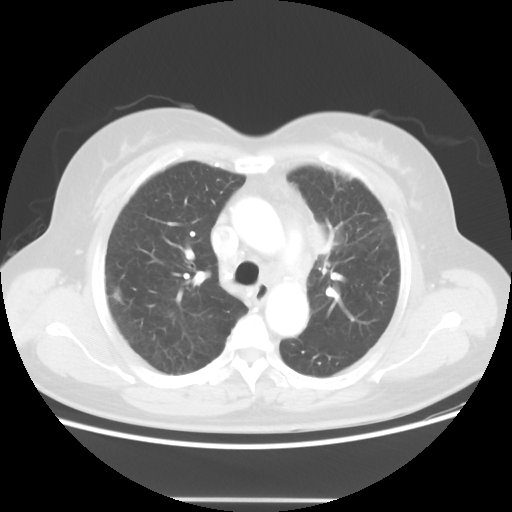
Chest CT, one axial slice; position 38 of 52 along the scan axis; reconstruction kernel STANDARD; 120 kVp; lung window (W 1500 / L -600 HU); 512 × 512 image matrix, field of view 382 × 382 mm. Female patient, age 52 years. From the clinical record (not read from this slice): clinical TNM (as recorded): T2 N3 M0.
Outlined on this slice (rectangle marked by the reading radiologist):
- lung tumour (recorded histology: adenocarcinoma): bounding box [x1, y1, x2, y2] px = [299, 207, 342, 260]